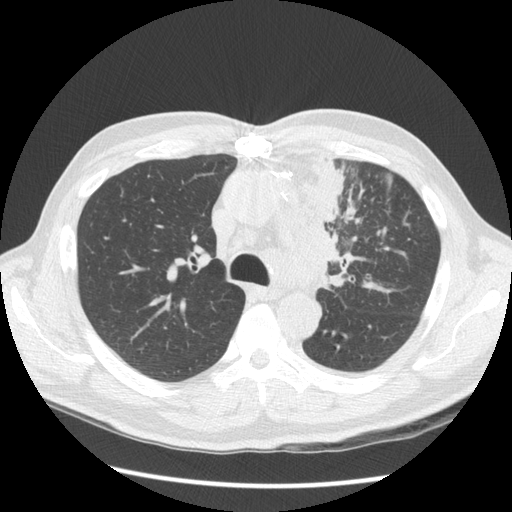
Low-dose screening chest CT, one axial slice; position 94 of 136 along the scan axis; reconstruction kernel STANDARD; 120 kVp; lung window (W 1500 / L -600 HU); 2.5 mm slice thickness; 512 × 512 image matrix, field of view 360 × 360 mm.
Structures marked on this image (manually delineated by an expert):
- lesion 1 (tumor, upper lobe of left lung): bounding box [x1, y1, x2, y2] px = [305, 152, 343, 296]